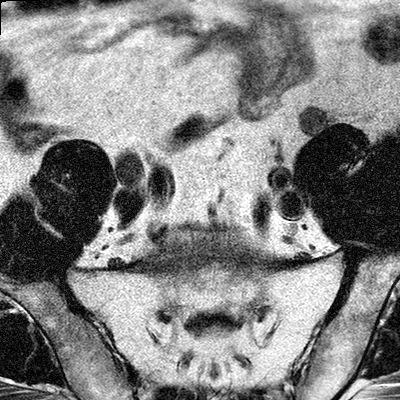
Multiparametric prostate MRI examination; 3 images, each a single mid-volume slice chosen by position (not for content). Treatment context recorded for this patient: No surgery, patient was keen on XRT/ADT.
Image 1: axial T2-weighted image, slice 17 of 32.
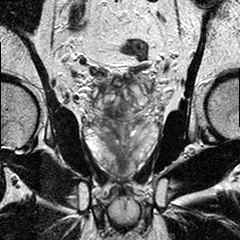
Image 2: coronal T2-weighted image, slice 13 of 24.
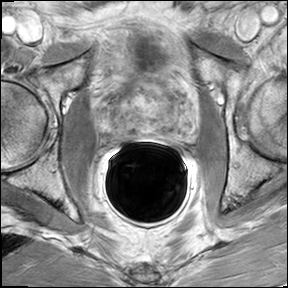
Image 3: DCE (dynamic gadolinium-enhanced) axial slice, slice 17 of 32, dynamic phase 5 of 8.
MRI report (verbatim):
FINDINGS: The prostate has a maximal lateral diameter of 5.0 cm, a maximal craniocaudal diameter of 4.6 cm and a maximal AP diameter of 3.5 cm resulting in an estimated gland volume of 42 cc. The zonal anatomy is preserved. There is a 1.6 x 1.2 cm geographic area of hypo intense signal seen on T2-weighed images, with suspicions wash in and wash out on the contrast enhanced dynamic series, in the right posterior lateral peripheral zone between 6-9 o'clock, with dominant nodule in the mid third of the prostate, which also involves adjacent areas of the central gland. The tumor extends into the base and apical third; at the level of the apical third, there is suspicious enhancement bilateral in the posterior aspects of the gland. There is no evidence of extraglandular extension. Late enhancement of diffuse centripetal pseudo septations diffuse in the peripheral zones of both sides, suggestive for chronic prostatitis. Nodularity in the central gland suggestive for BPH. No evidence for involvement of the neurovascular bundle on either side. No evidence for seminal vesicles infiltration. No evidence of involvement of bladder neck and rectal wall. No suspiciously enlarged obturator and iliac lymph nodes. IMPRESSION: Bilateral Tumor with dominant nodule in the right peripheral zone, in the mid third of the prostate, as detailed above. No evidence of extraglandular extension. No evidence of seminal vesicle infiltration or involvement of the neurovascular bundle on either side. No pelvic lymphadenopathy. Moderate chronic prostatitis. Moderate BPH. Incidental note is made of sigma diverticulosis.

Prostate biopsy pathology (as recorded):
The specimen consists of multiple core fragments of tan soft tissue measuring 0.2cm to 1.7cm in length and 0.1cm in diameter. The specimen is submitted entirely in six cassettes as follows: 1-right PZ, 2-right PZ TZ, 3-right apex, 4-left PZ, 5-left PZ TZ, 6-left apex. PROSTATE BIOPSIES: 1. RIGHT PZ: PROSTATIC TISSUE, NO TUMOR IDENTIFIED. 2. RIGHT PZ/TZ: PROSTATIC ADENOCARCINOMA, GLEASON SCORE 3+4=7/10, PRESENT IN TWO TISSUE CORES (10% OF TISSUE). PROSTATIC TISSUE, NO TUMOR IDENTIFIED. 3. RIGHT APEX: PROSTATIC ADENOCARCINOMA, GLEASON SCORE 3+4=7/10, PRESENT IN TWO TISSUE CORES (30% OF TISSUE). 4. LEFT PZ: PROSTATIC ADENOCARCINOMA, GLEASON SCORE 3+4=7/10, PRESENT IN ONE TISSUE CORE (10% OF TISSUE). 5. LEFT PZ/TZ: PROSTATIC TISSUE, NO TUMOR IDENTIFIED. 6. LEFT APEX: MICROSCOPIC FOCUS OF PROSTATIC ADENOCARCINOMA, GLEASON SCORE 3+3=6/10, (<1% OF TISSUE). PIN-4 IMMUNOHISTOCHEMISTRY CONFIRMS THE DIAGNOSIS